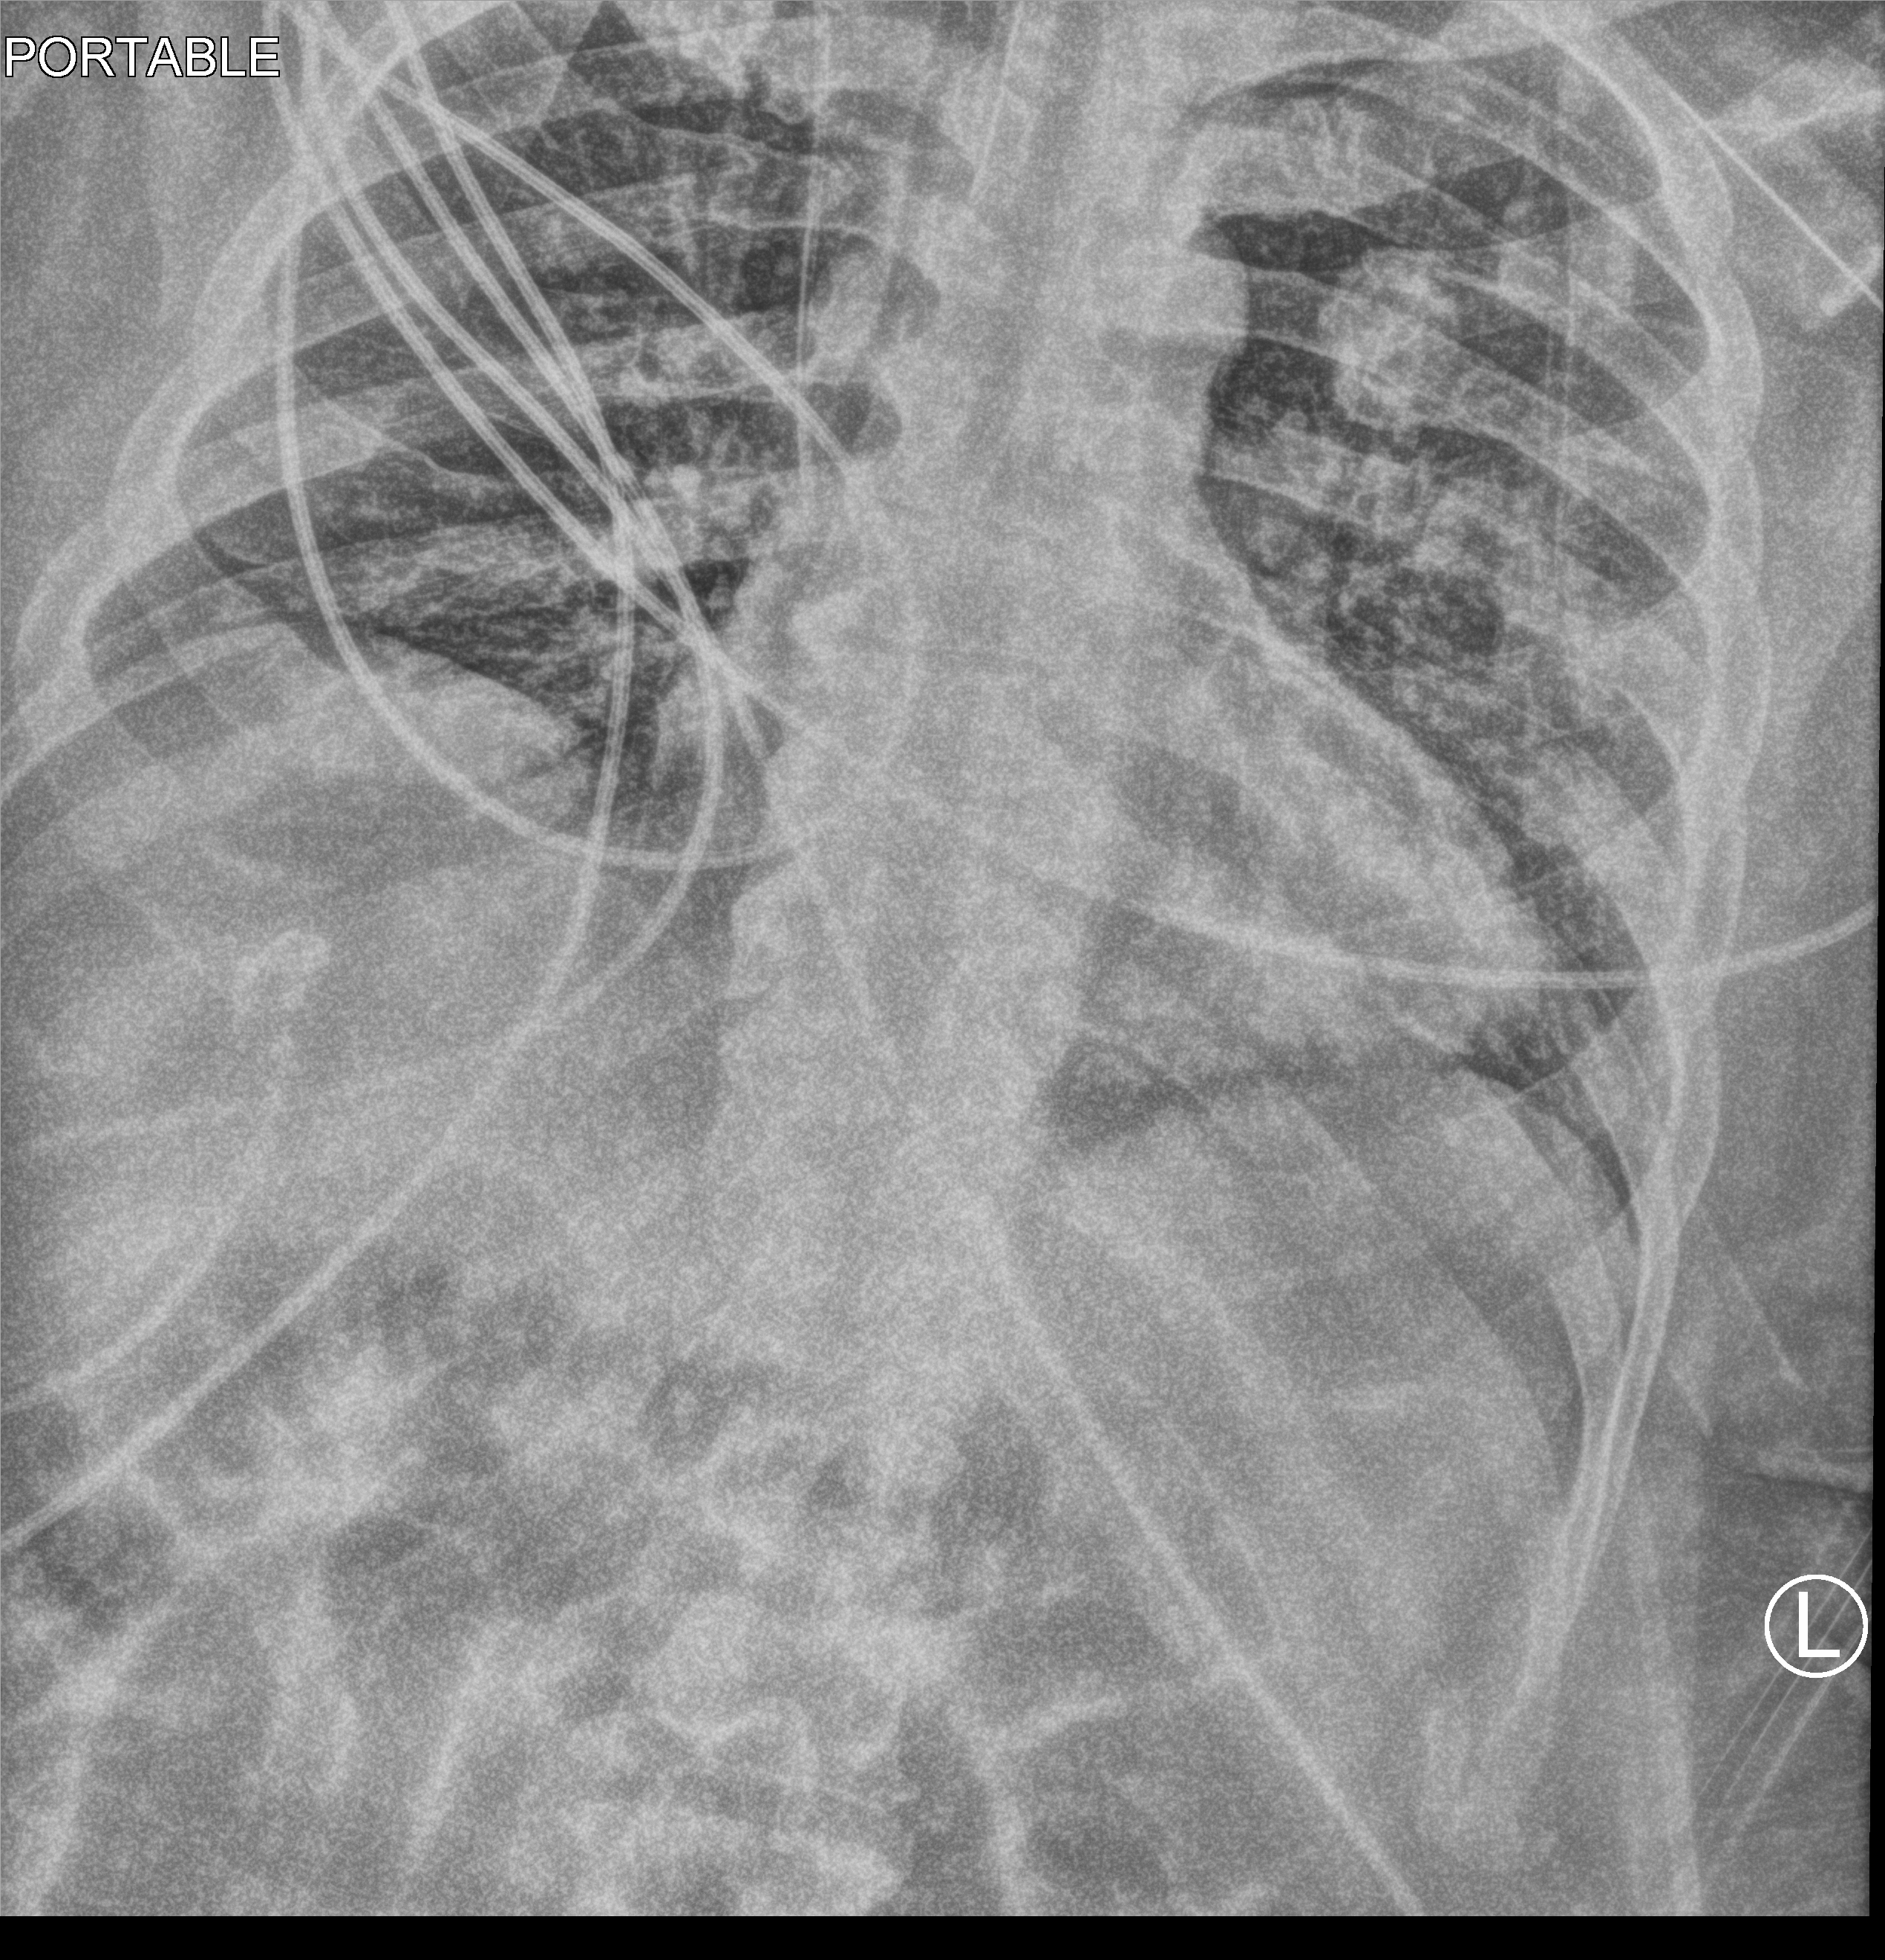
Portable chest radiograph, anteroposterior (AP) projection. Male patient hospitalised with COVID-19, age 18–59 years.
Hospital-stay facts (about this admission, not read from this image; timing relative to this image not recorded): mechanically ventilated during this hospital stay: yes.